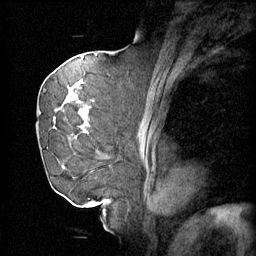
Breast MRI (dynamic contrast-enhanced), one sagittal slice; position 32 of 60 along the scan axis; 4 images stored at this slice position (order not interpretable as contrast timing); 1.5 T; TE 4.2 ms, TR 11 ms; 2 mm slice thickness; 256 × 256 image matrix, field of view 220 × 220 mm. Female patient, age 72 years.
Structures marked on this image (semi-automatically segmented with operator editing):
- analysis volume of interest (the breast-tissue region the enhancement analysis was run in; not a lesion): box from (x=43, y=68) to (x=109, y=163) px
- tumour enhancement mask (voxels above the 70 % enhancement threshold inside the analysis volume of interest): (x=44, y=74)–(x=96, y=135)